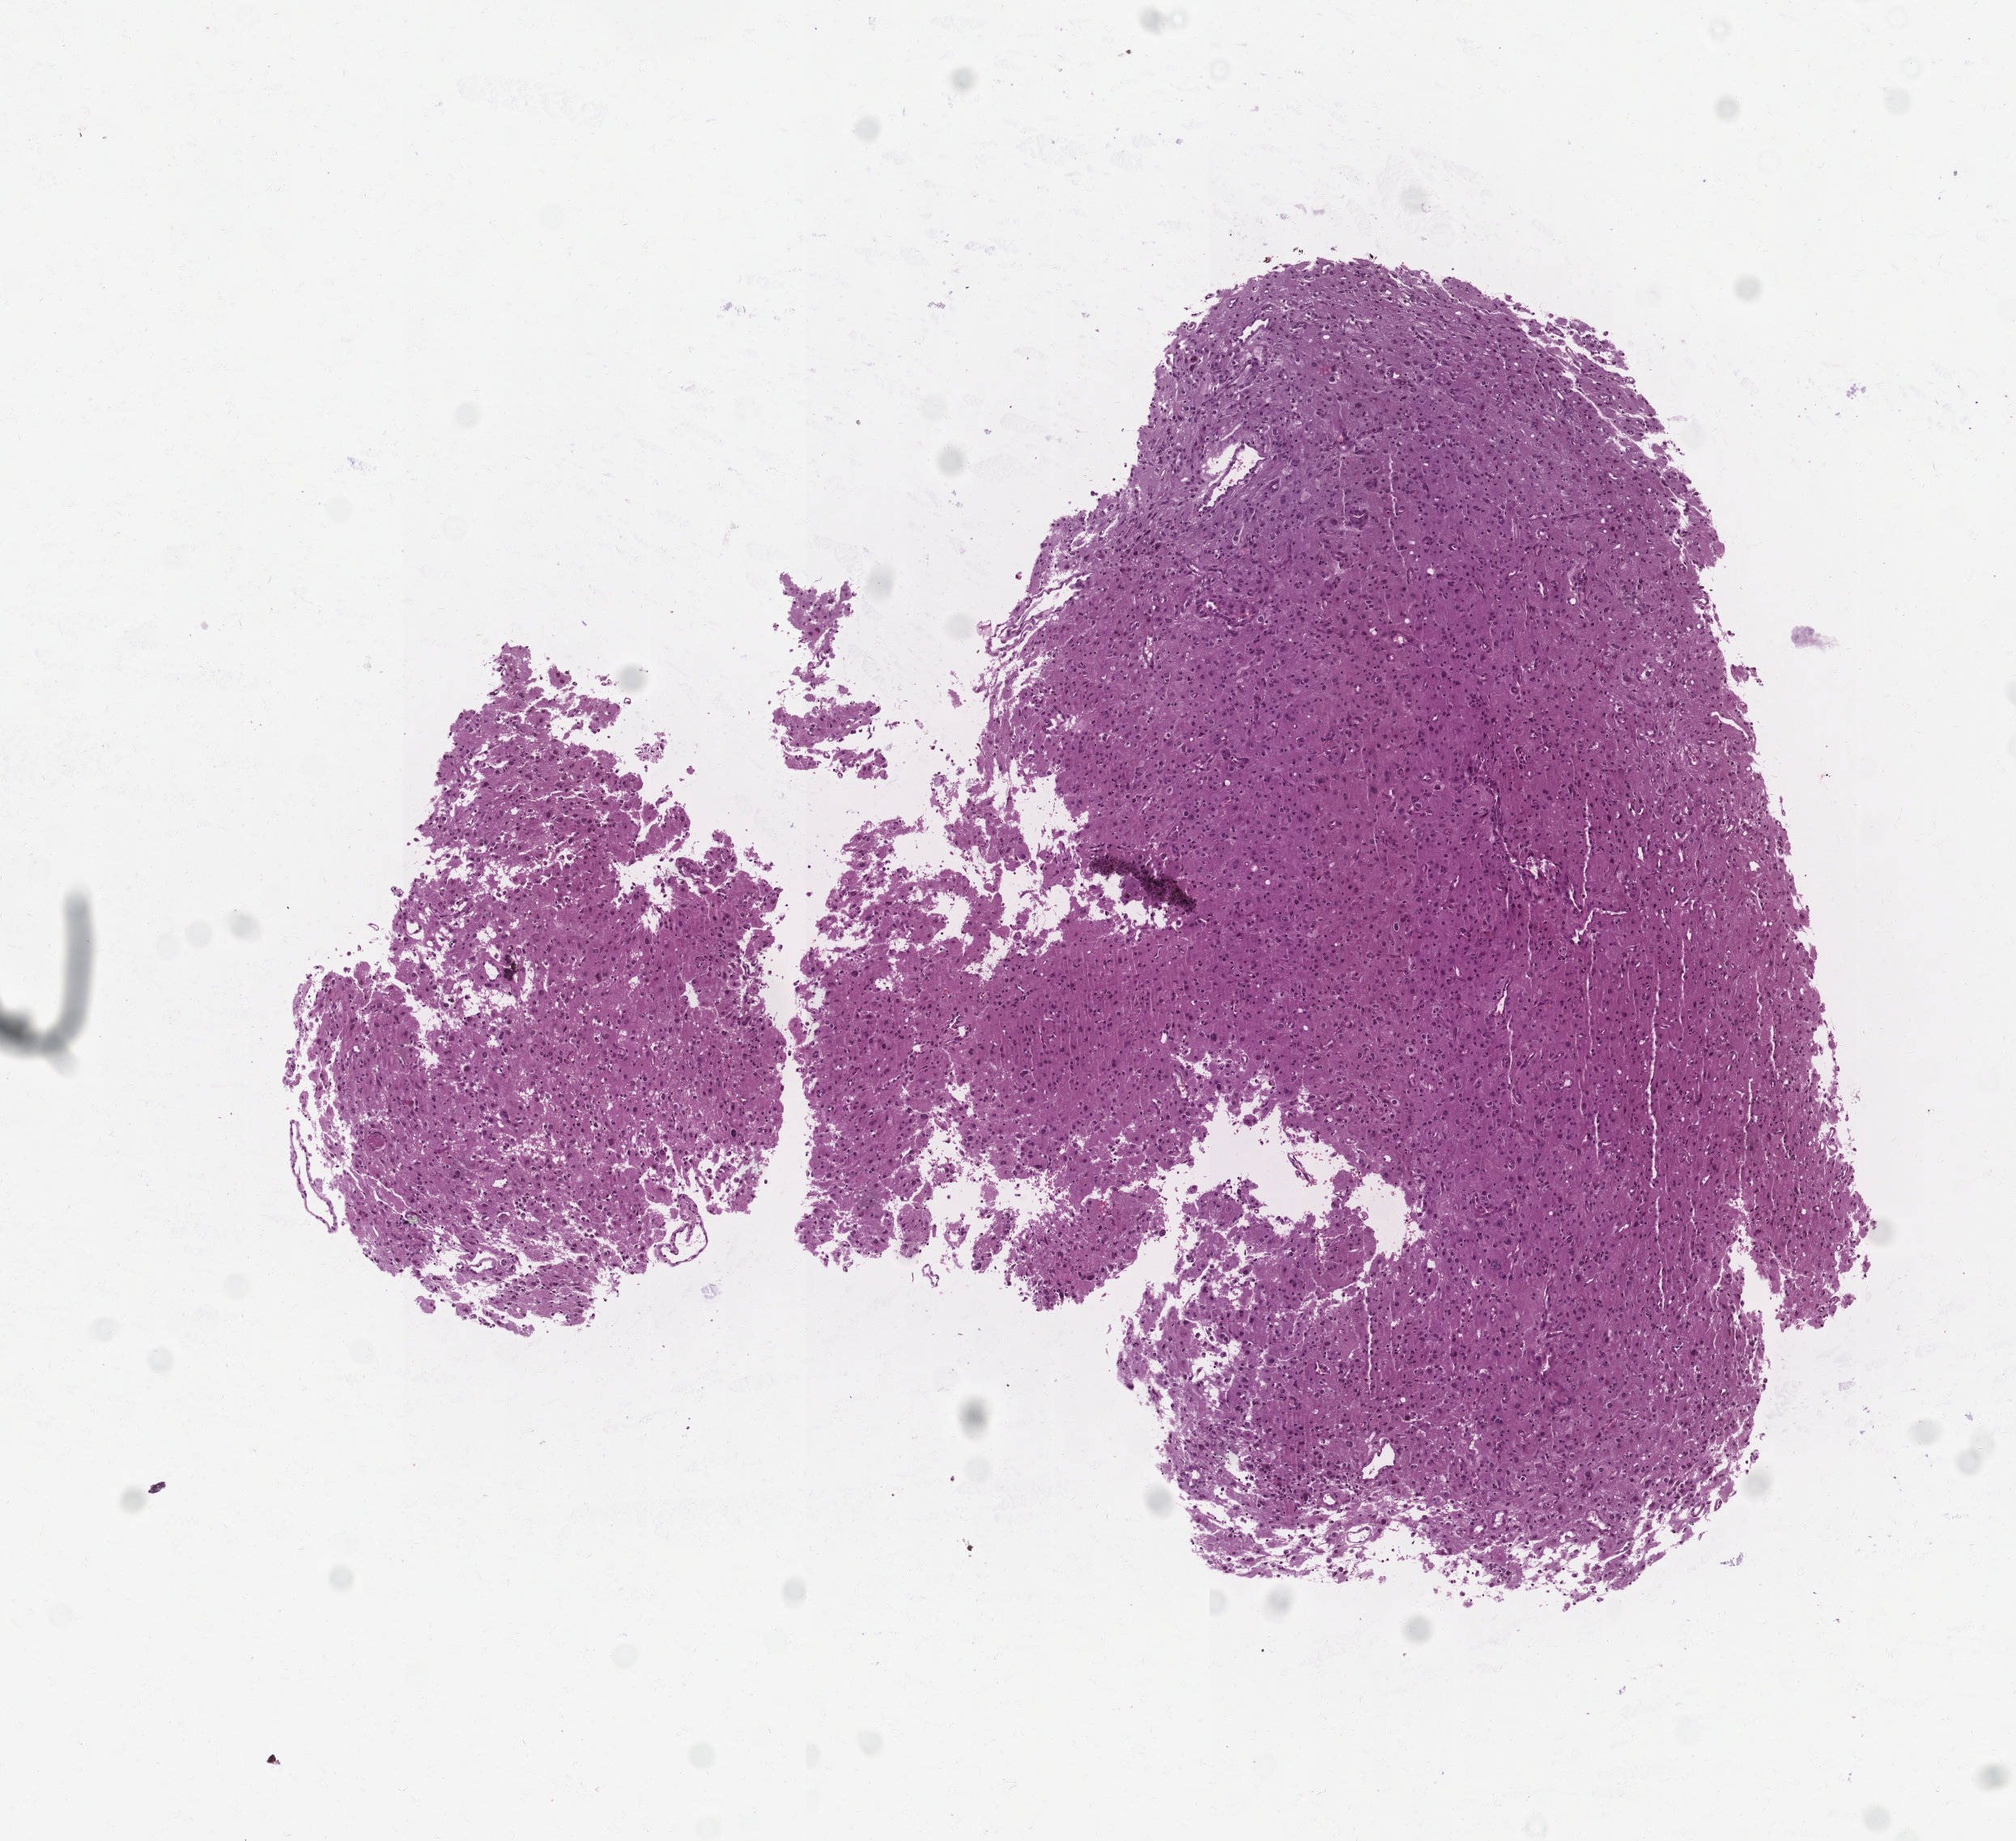
Digitized H&E-stained tissue section (whole slide) — a low-resolution overview of the entire scanned area, about 5.0 x 4.6 mm; tumour tissue sample, sampled site: brain. Patient: male, age 35 years. Pathologist review of this section (percent, as recorded): tumour nuclei 85%, necrosis 5%.
Histologic diagnosis: Glioblastoma.